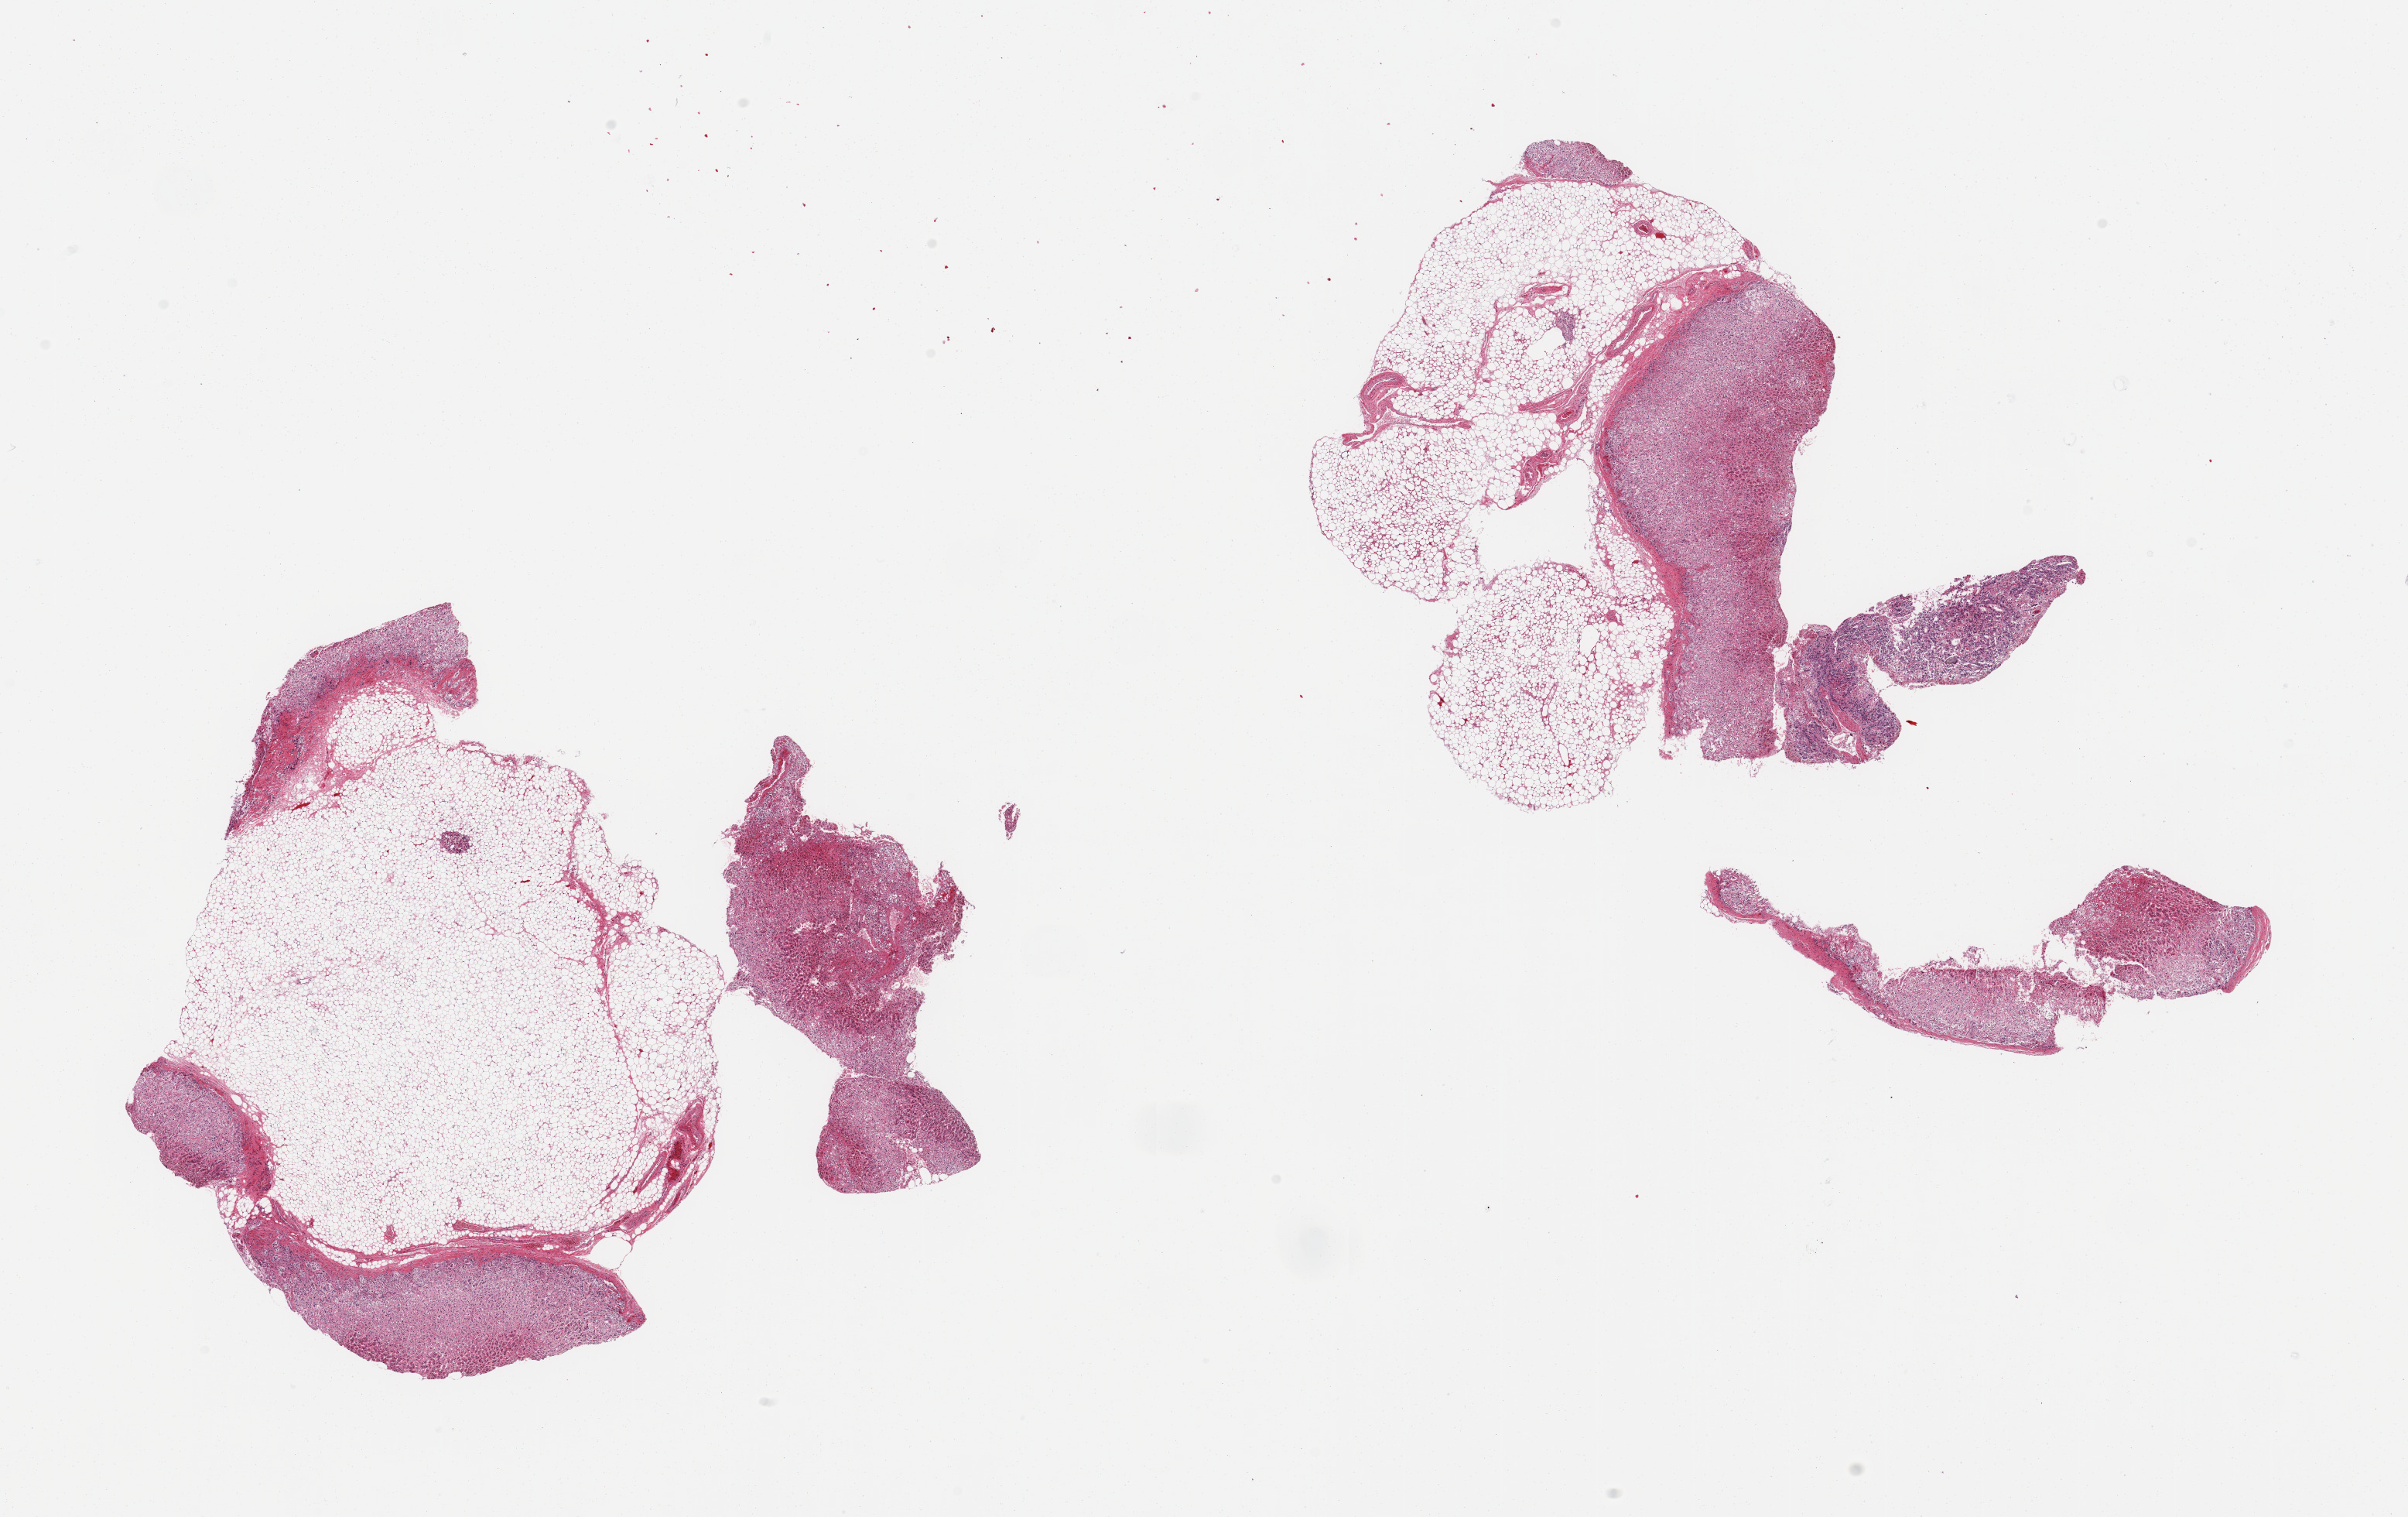
Digitized hematoxylin and eosin (H&E)-stained section, brightfield — whole scanned area (about 24.6 x 15.5 mm, slide scanned at 20x) shown as a low-resolution overview, PAXgene-fixed, paraffin-embedded tissue, section of adrenal gland (target tissue), donor tissue sample. Donor sex: female.
Review note (as recorded): 2 pieces( fragmented), ~60% adherent interstitial fat; 40% corte.